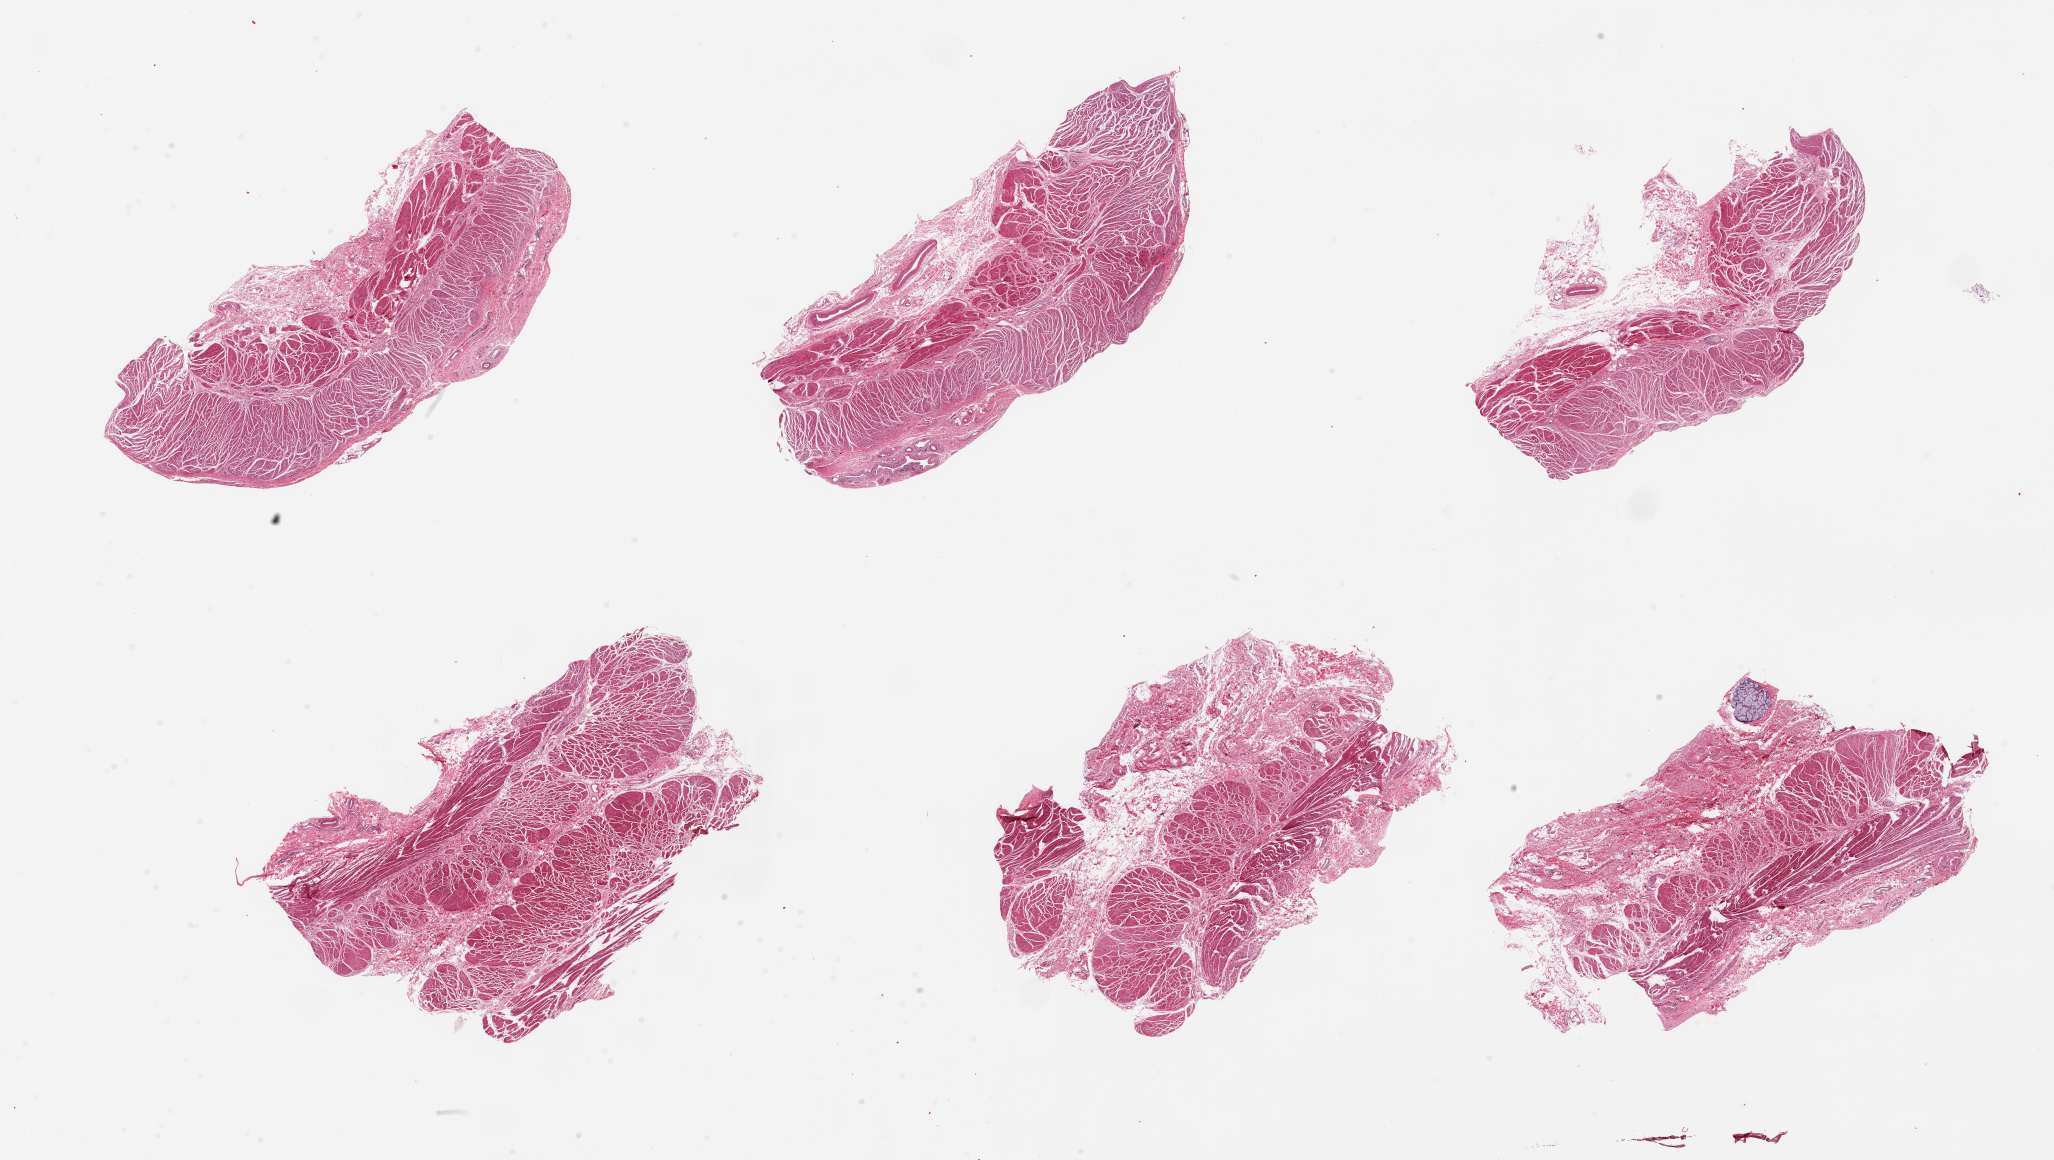
H&E whole-slide image, low-resolution overview of the scanned area, about 32.5 x 18.3 mm (acquisition: 20x scan), PAXgene-fixed paraffin-embedded (PFPE) section, section of gastroesophageal junction (target tissue), donor tissue sample. Donor: female.
Review note (as recorded): 6 pieces; 0.6 mm submucosal gland in 1 piece.